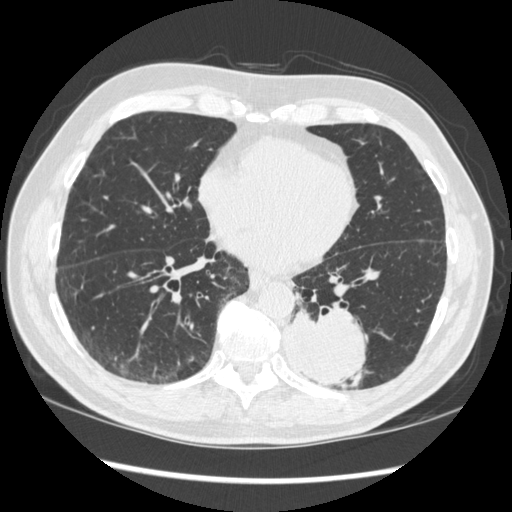
Low-dose screening chest CT, one axial slice; reconstruction kernel STANDARD; lung window (W 1500 / L -600 HU); 1.25 mm slice thickness; 512 × 512 image matrix, field of view 360 × 360 mm.
Annotated regions visible in this slice (expert manual segmentation):
- lesion 1 (tumor, lower lobe of left lung): box from (x=284, y=311) to (x=367, y=389) px